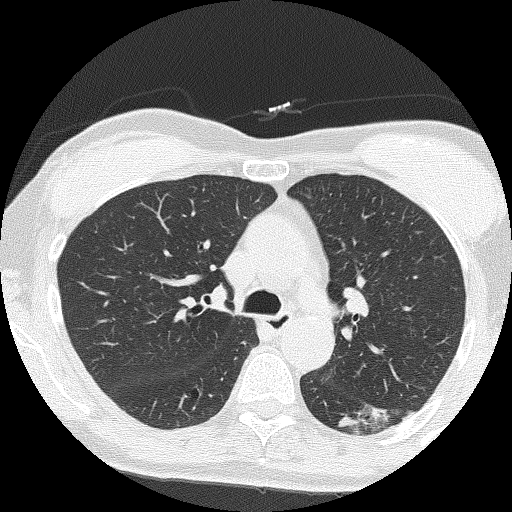
Chest CT (low-dose screening protocol), one axial image, second annual screen, lung window (W 1500 / L -600 HU), 2 mm slice thickness, 120 kVp. Female, age 64 years at enrolment.
Lesion marked by an expert reader, bounding box [x1, y1, x2, y2] px = [354, 392, 415, 440]. The screening reader recorded 3 non-calcified nodules or masses ≥4 mm on this exam (right upper lobe, right upper lobe, right middle lobe); which of them this box marks is not recorded. Official screen result: positive, other. Participant outcome: lung cancer diagnosed 576 days after this screen — adenocarcinoma, NOS, left lower lobe, moderately differentiated (G2), stage IA (AJCC 6th edition), 17 mm at pathology.